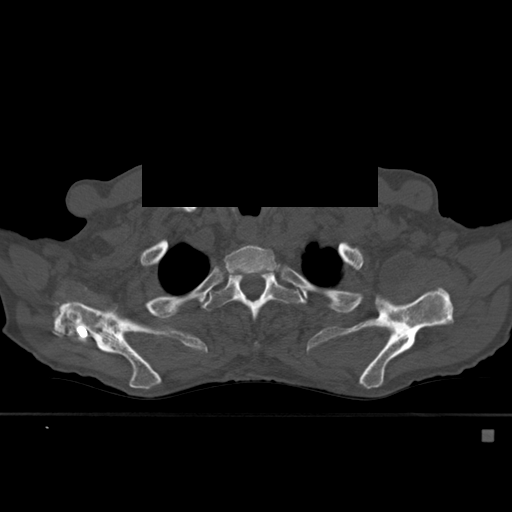
CT including the spine, one axial slice. Position 437 of 527 along the scan axis. Bone window (W 1800 / L 400 HU). 1.5 mm slice thickness. 512 × 512 image matrix. Male patient, age 78 years. From the clinical record (not read from this slice): primary cancer: prostate.
Structures marked on this image (semi-automatically segmented with operator editing):
- T2 vertebra: bounding box <223,245,276,281> (left, top, right, bottom; pixels)
- T3 vertebra: <202,273,302,350>